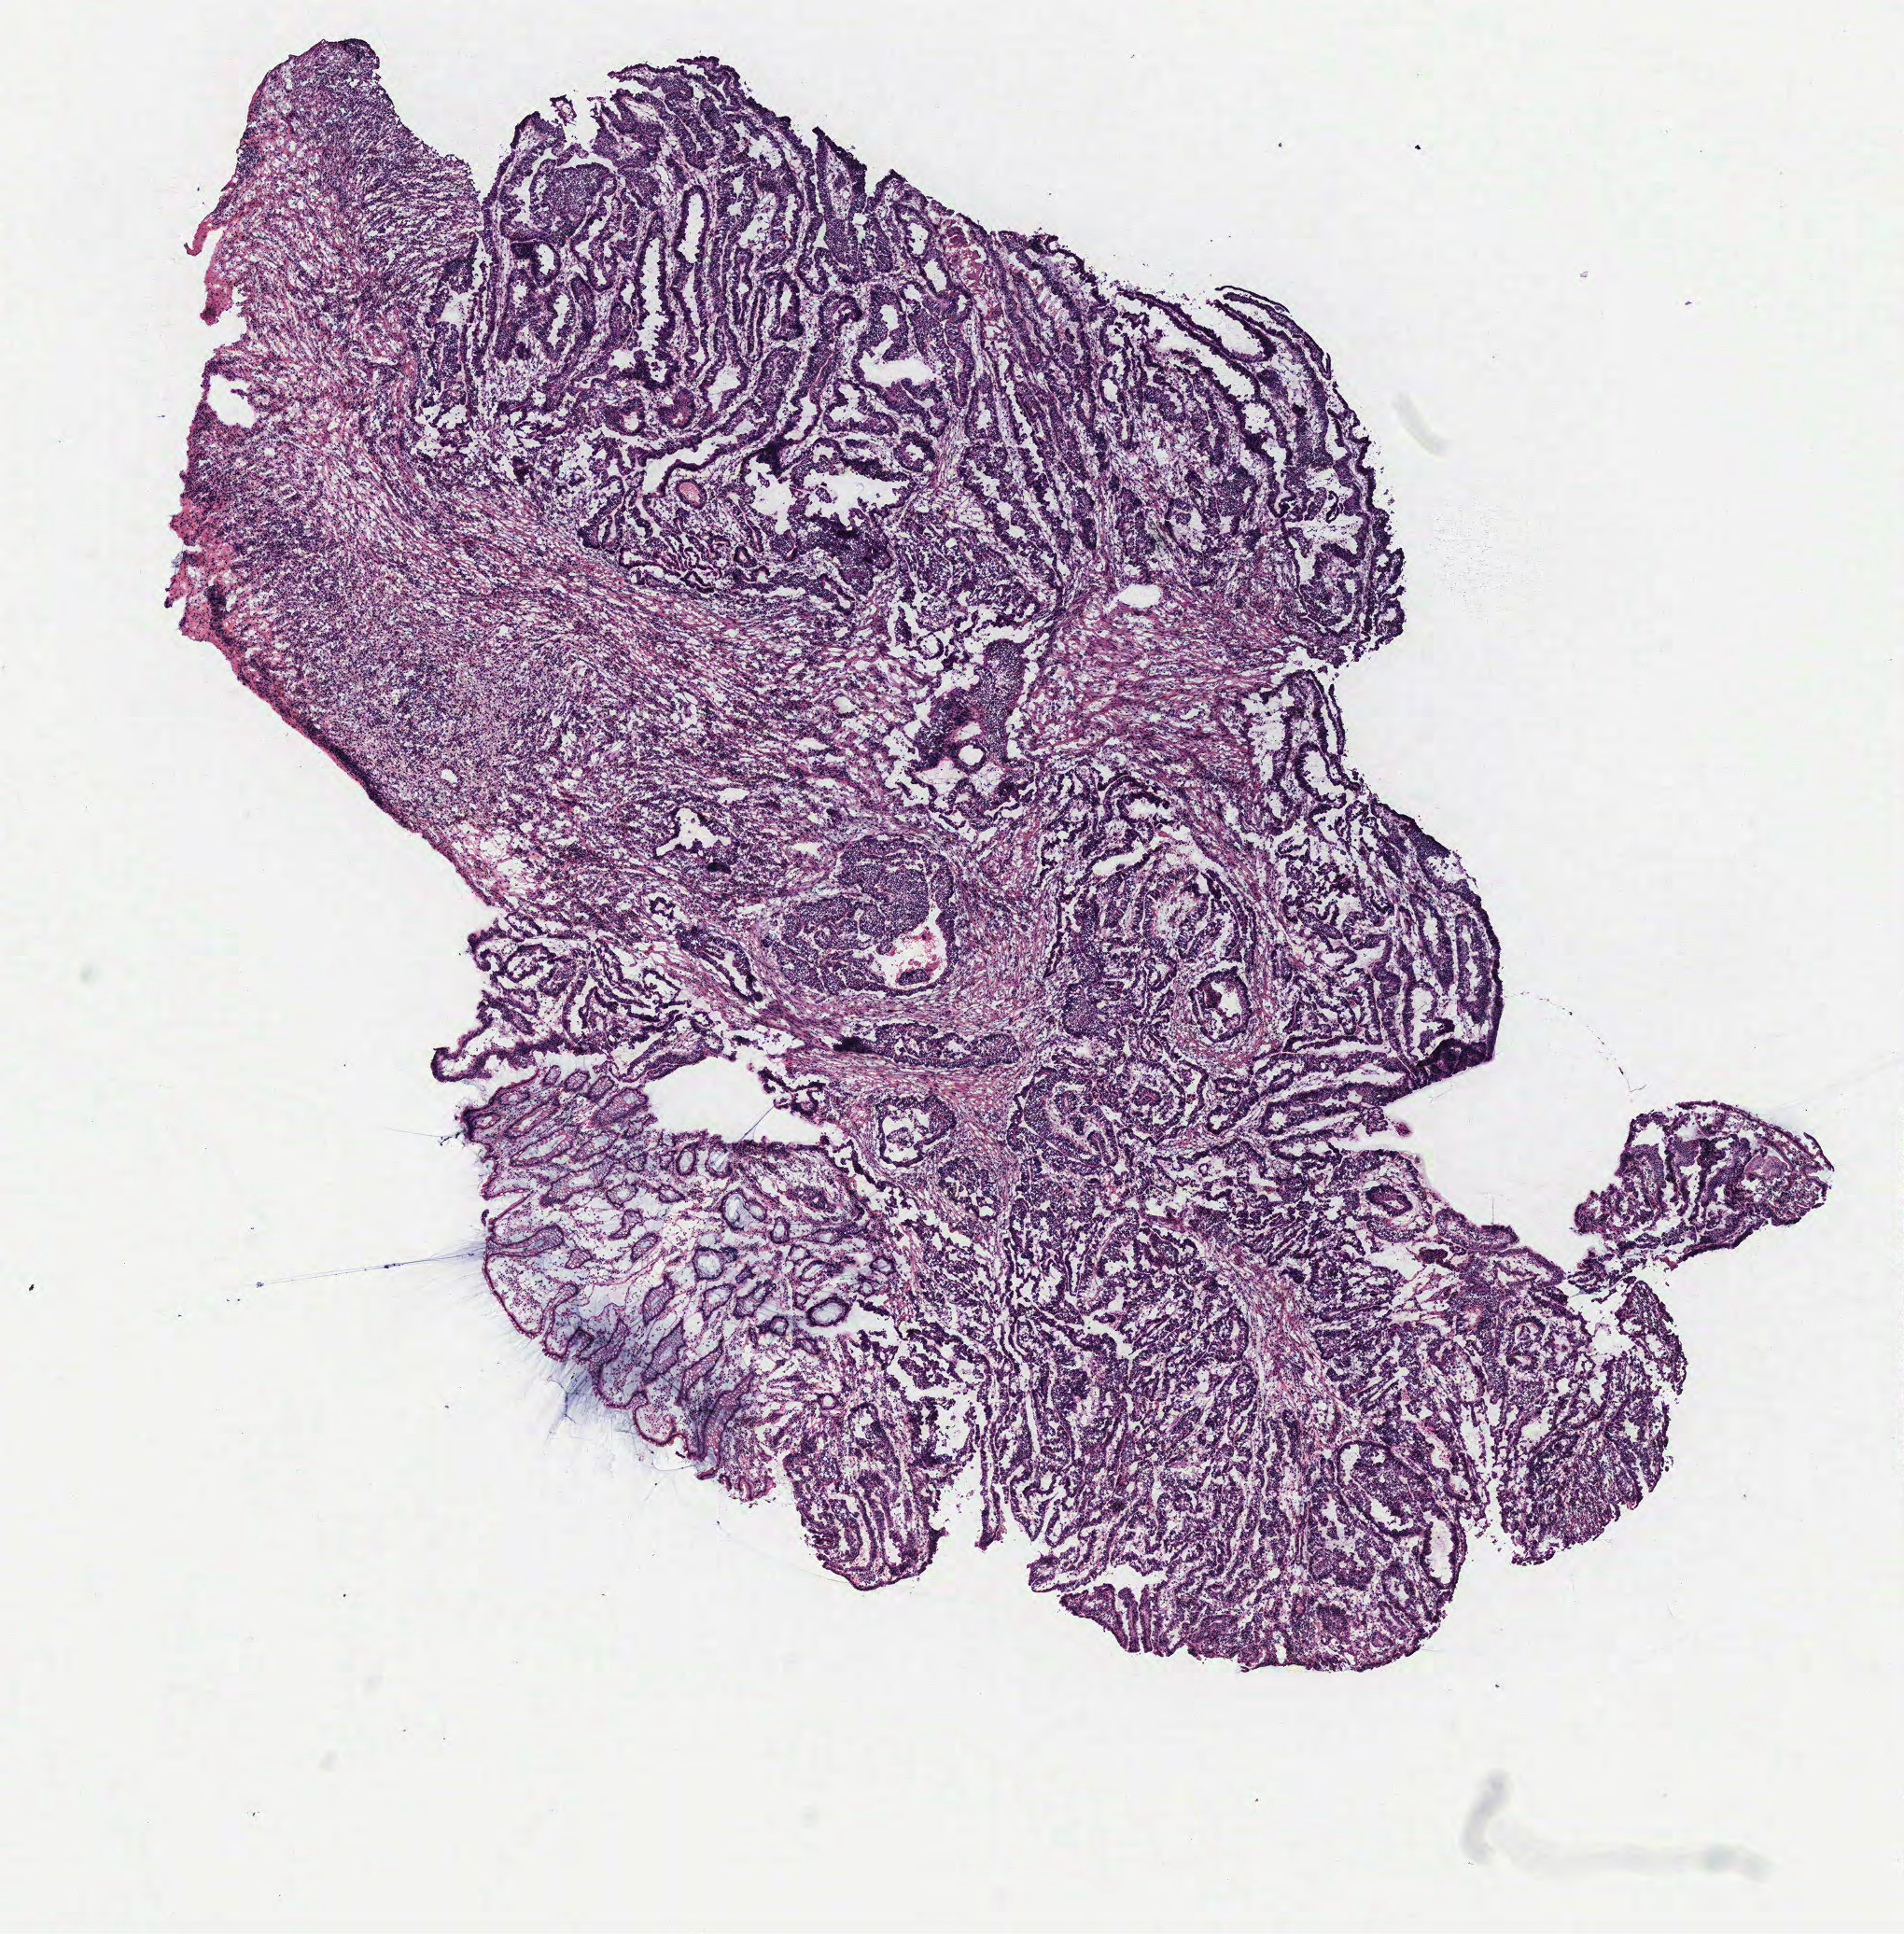
Hematoxylin and eosin (H&E) stained whole-slide image, a low-resolution overview of the entire scanned area, about 8.2 x 8.3 mm (slide scanned at 40x). Normal (non-tumour) tissue sample, colon. Male, 51 y/o.
* this section: normal (non-tumour) tissue from the same patient
* patient diagnosis: Adenocarcinoma, NOS